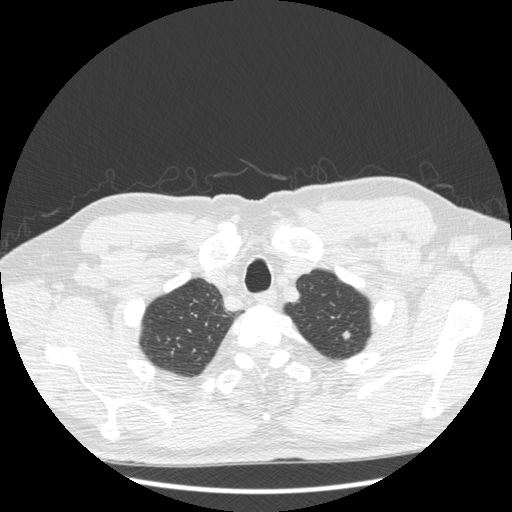
Low-dose screening chest CT, axial slice; third annual screen; lung window (W 1500 / L -600 HU); 1.25 mm slice thickness; 512 × 512 image matrix. Male, age 69 years at enrolment. Former smoker at enrolment.
- Expert-annotated lung lesion, bounding box <331,322,359,346> (left, top, right, bottom; pixels).
- The exam's reader record, not a measurement of the box and not confirmed to be the same lesion: non-calcified nodule or mass ≥4 mm, left upper lobe, 7 × 6 mm, smooth margins, soft tissue attenuation, pre-existing on the prior screen: yes; interval growth: yes.
- Official screen result: positive, other.